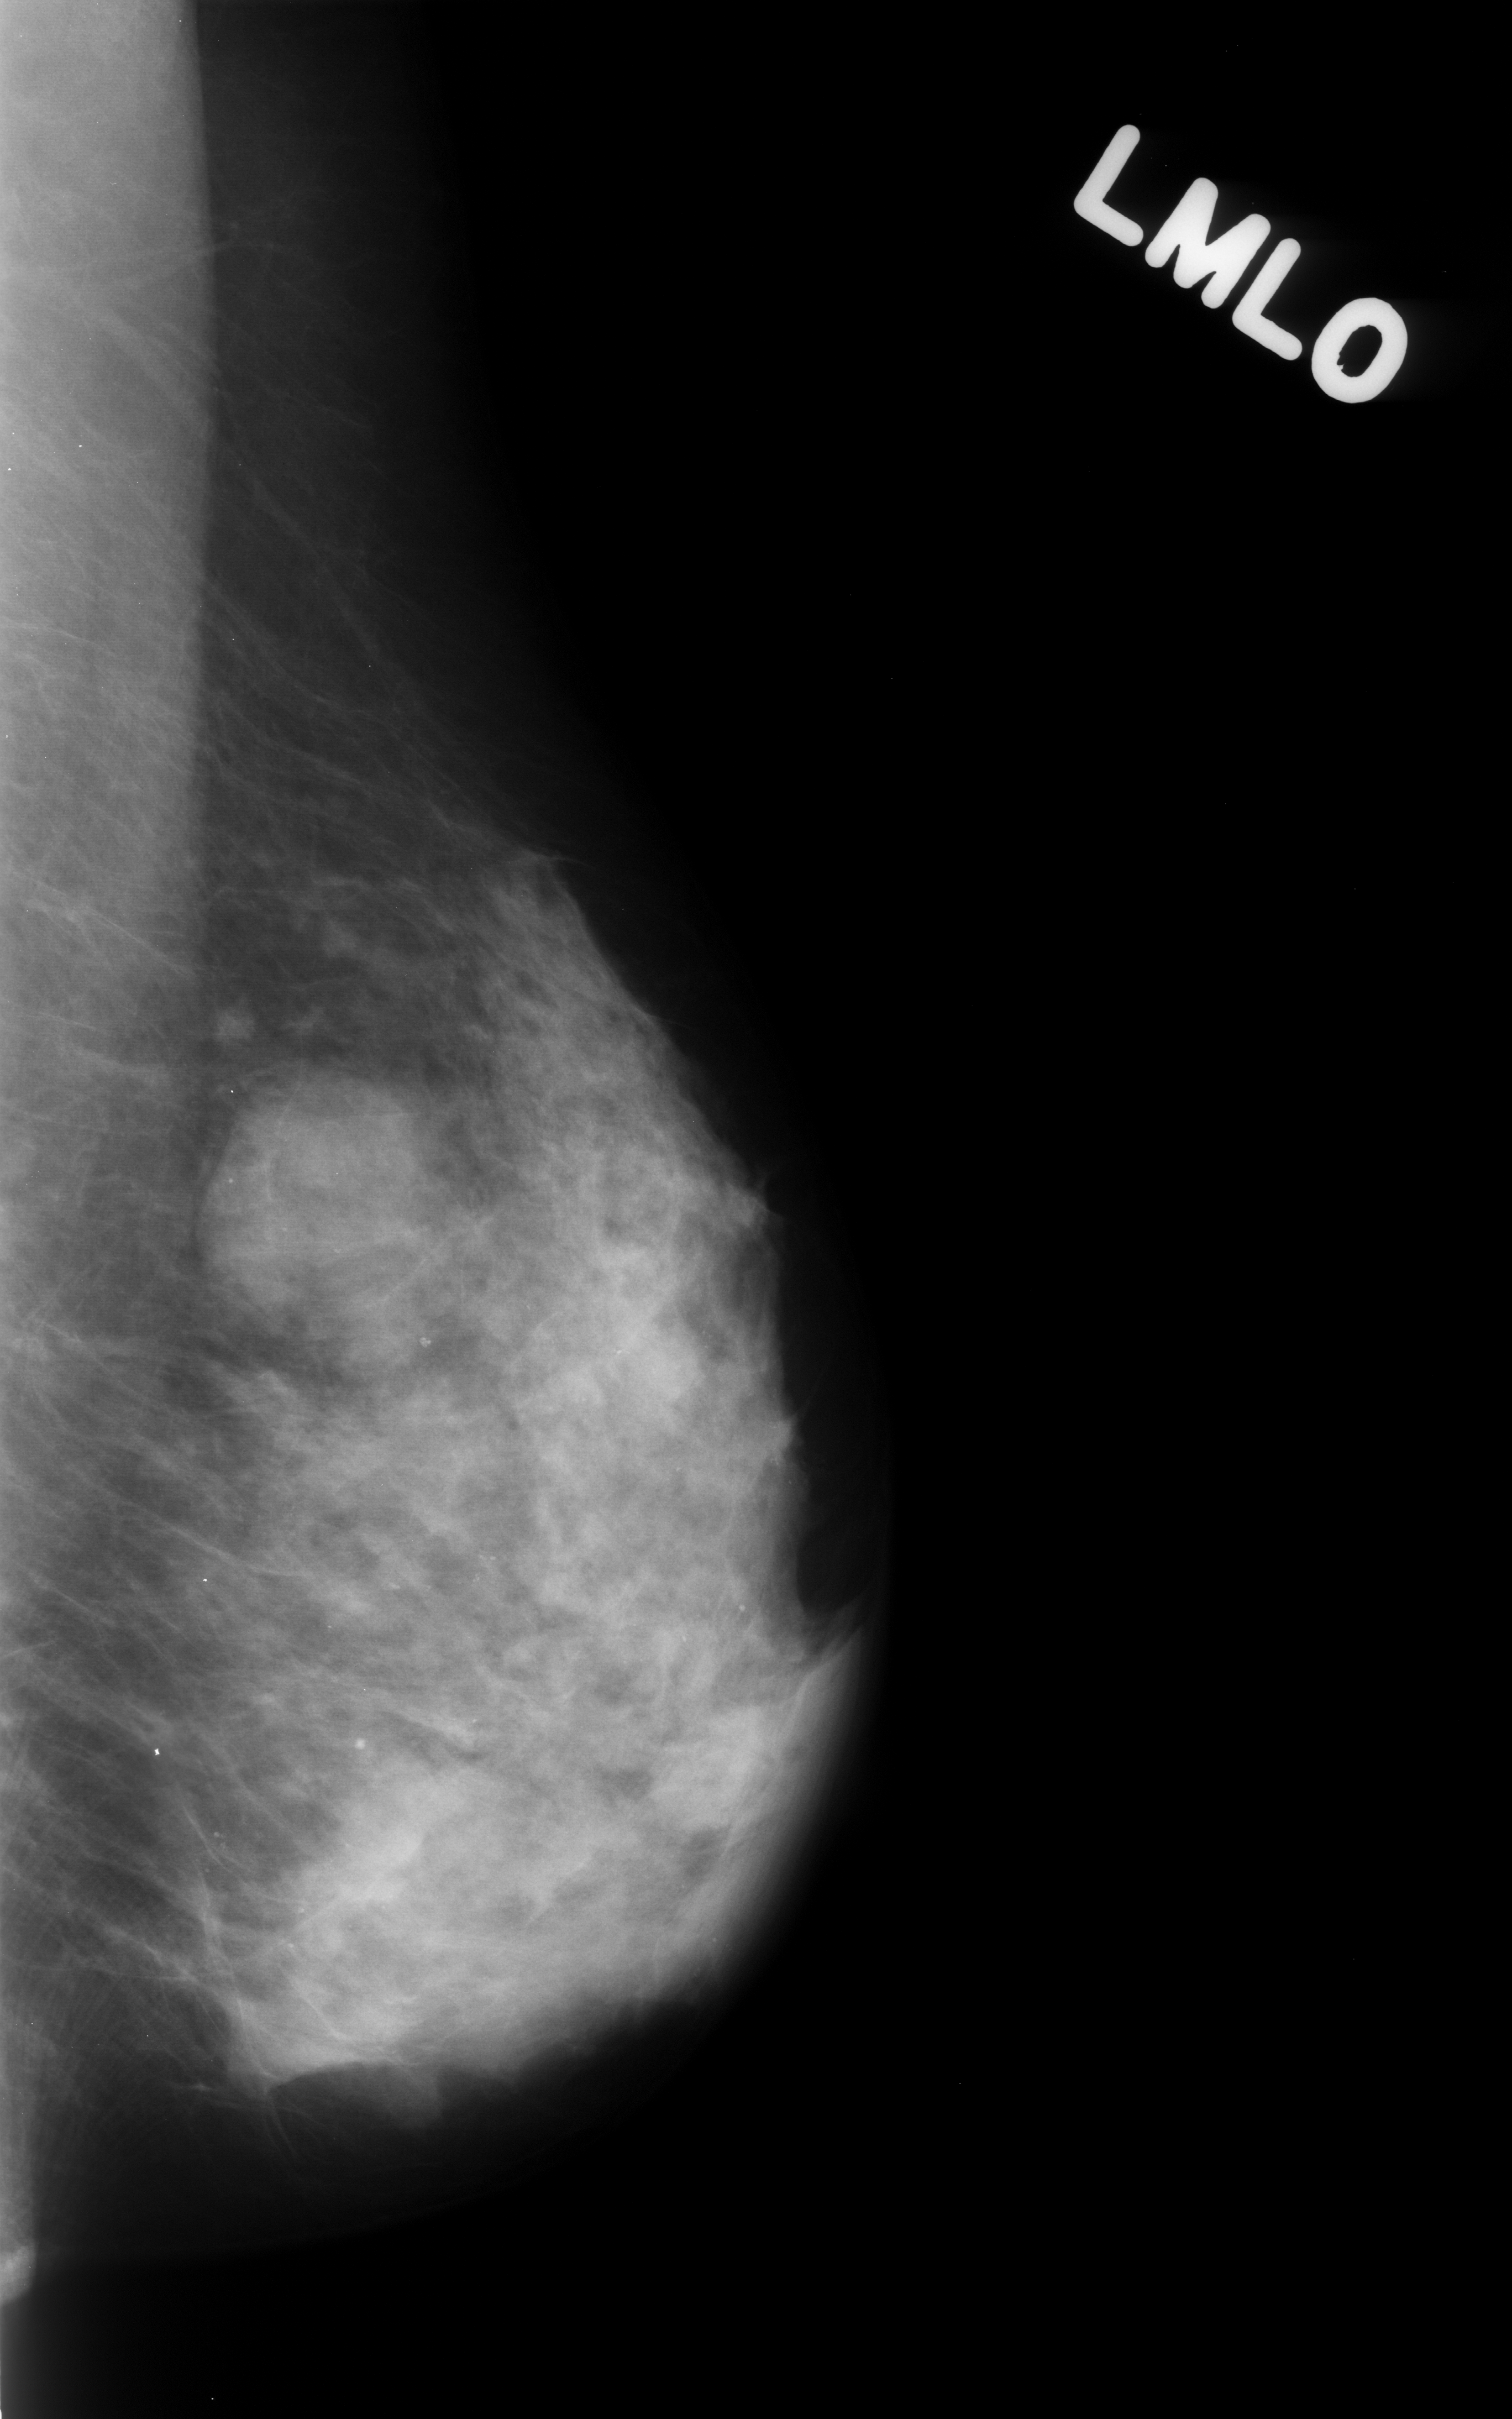
Scanned film-screen mammogram. Left breast. MLO view. Breast composition: heterogeneously dense (BI-RADS density category 3 of 4). 1512 × 2419 image matrix.
Expert-marked regions of interest on this image (one box per marked abnormality):
- calcifications, morphology pleomorphic, distribution diffusely scattered; BI-RADS assessment category 3; subtlety rating 3 on a 1 (subtle) to 5 (obvious) scale; pathology (as recorded): benign: bounding box (x1, y1, x2, y2) in pixels: (0, 981, 806, 2088)